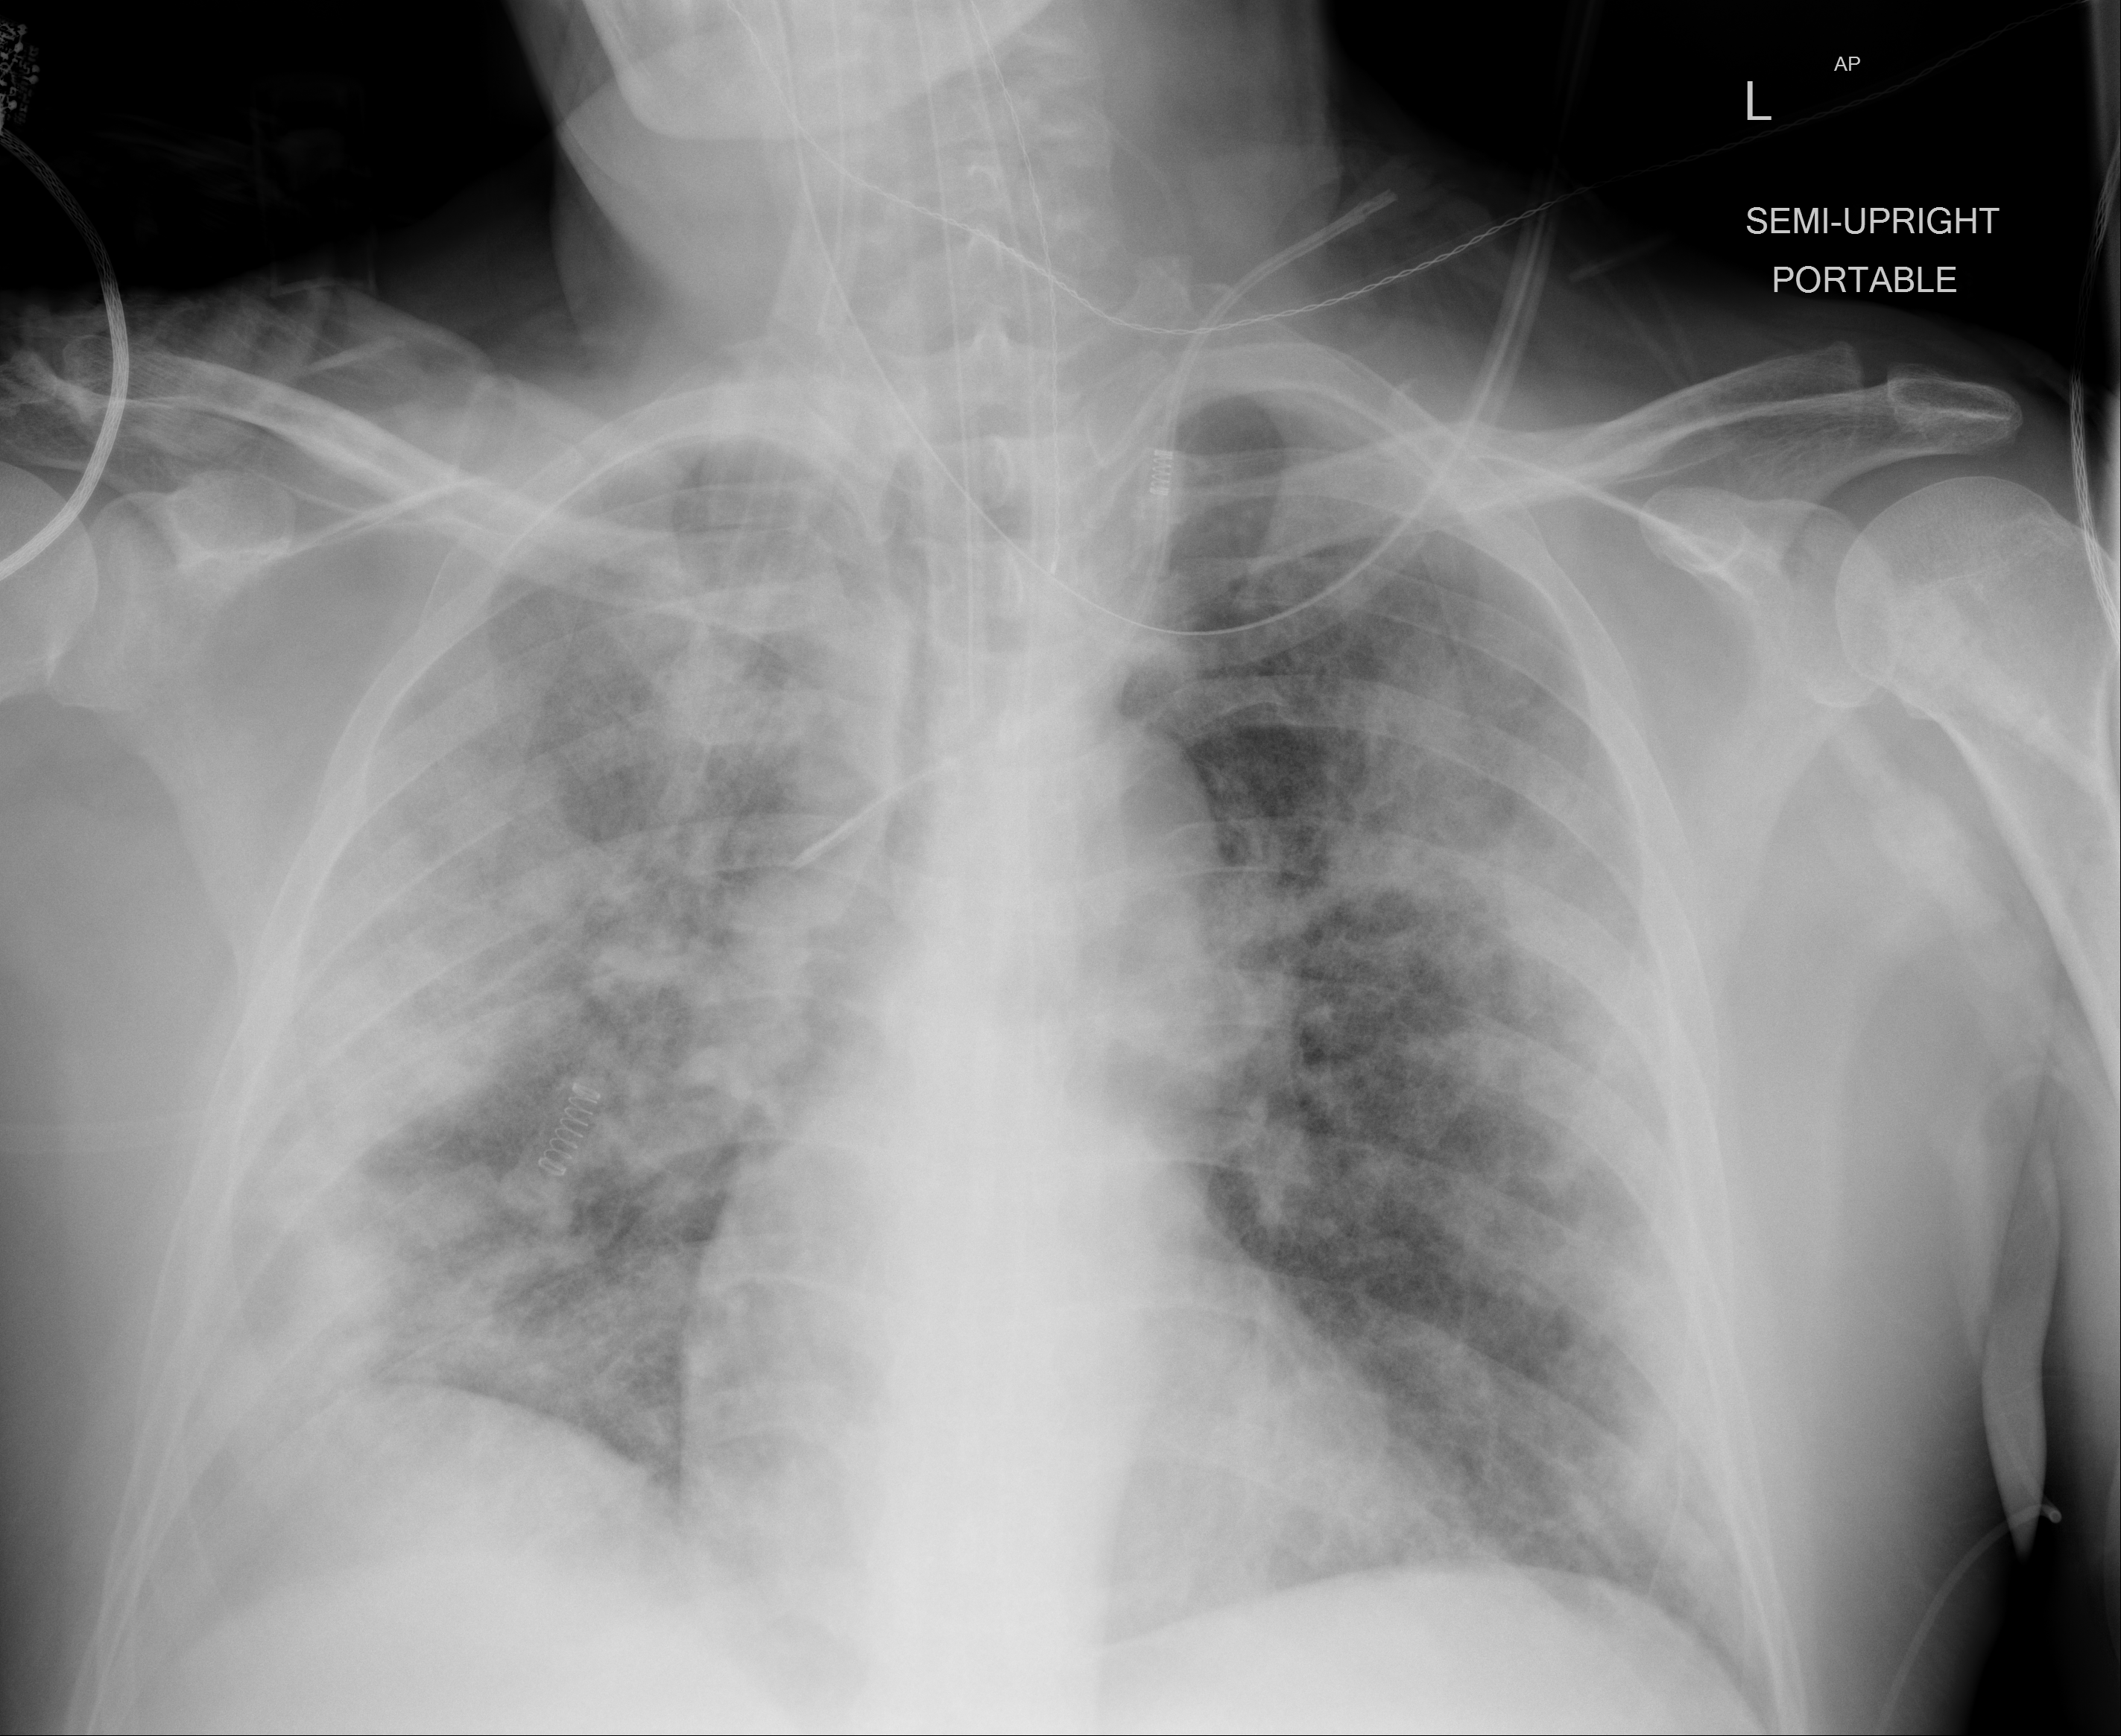
Chest X-ray, AP projection. Male patient, age 57 years; imaged 11 days after the COVID-19 diagnosis.
Radiologist key findings (as recorded): Multiple predominately peripheral infiltrates are seen throughout both lungs, somewhat more extensive in the right lung compared to the left.